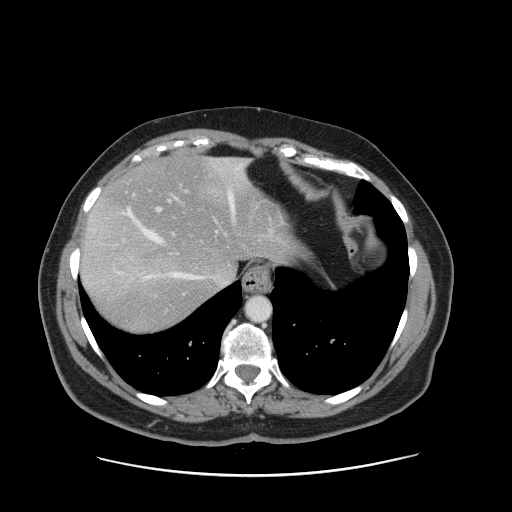
Contrast-enhanced abdominal CT, one axial slice; position 125 of 161 along the scan axis; soft-tissue window (W 400 / L 40 HU); 2.5 mm slice thickness; 512 × 512 image matrix. Female patient, age 62 years. Case-level facts recorded for this patient, not image findings: diagnosis: colorectal cancer liver metastases, imaged before liver resection; multiple liver metastases: no; largest metastasis: 2.5 cm; chemotherapy before resection: yes.
Structures marked on this image (expert manual segmentation):
- hepatic veins: bounding box (x1, y1, x2, y2) in pixels: (117, 167, 241, 283)
- liver: (81, 158, 295, 330)
- planned liver remnant (the part of the liver to remain after resection): (95, 157, 292, 279)
- portal vein (with intrahepatic branches): (156, 190, 273, 236)